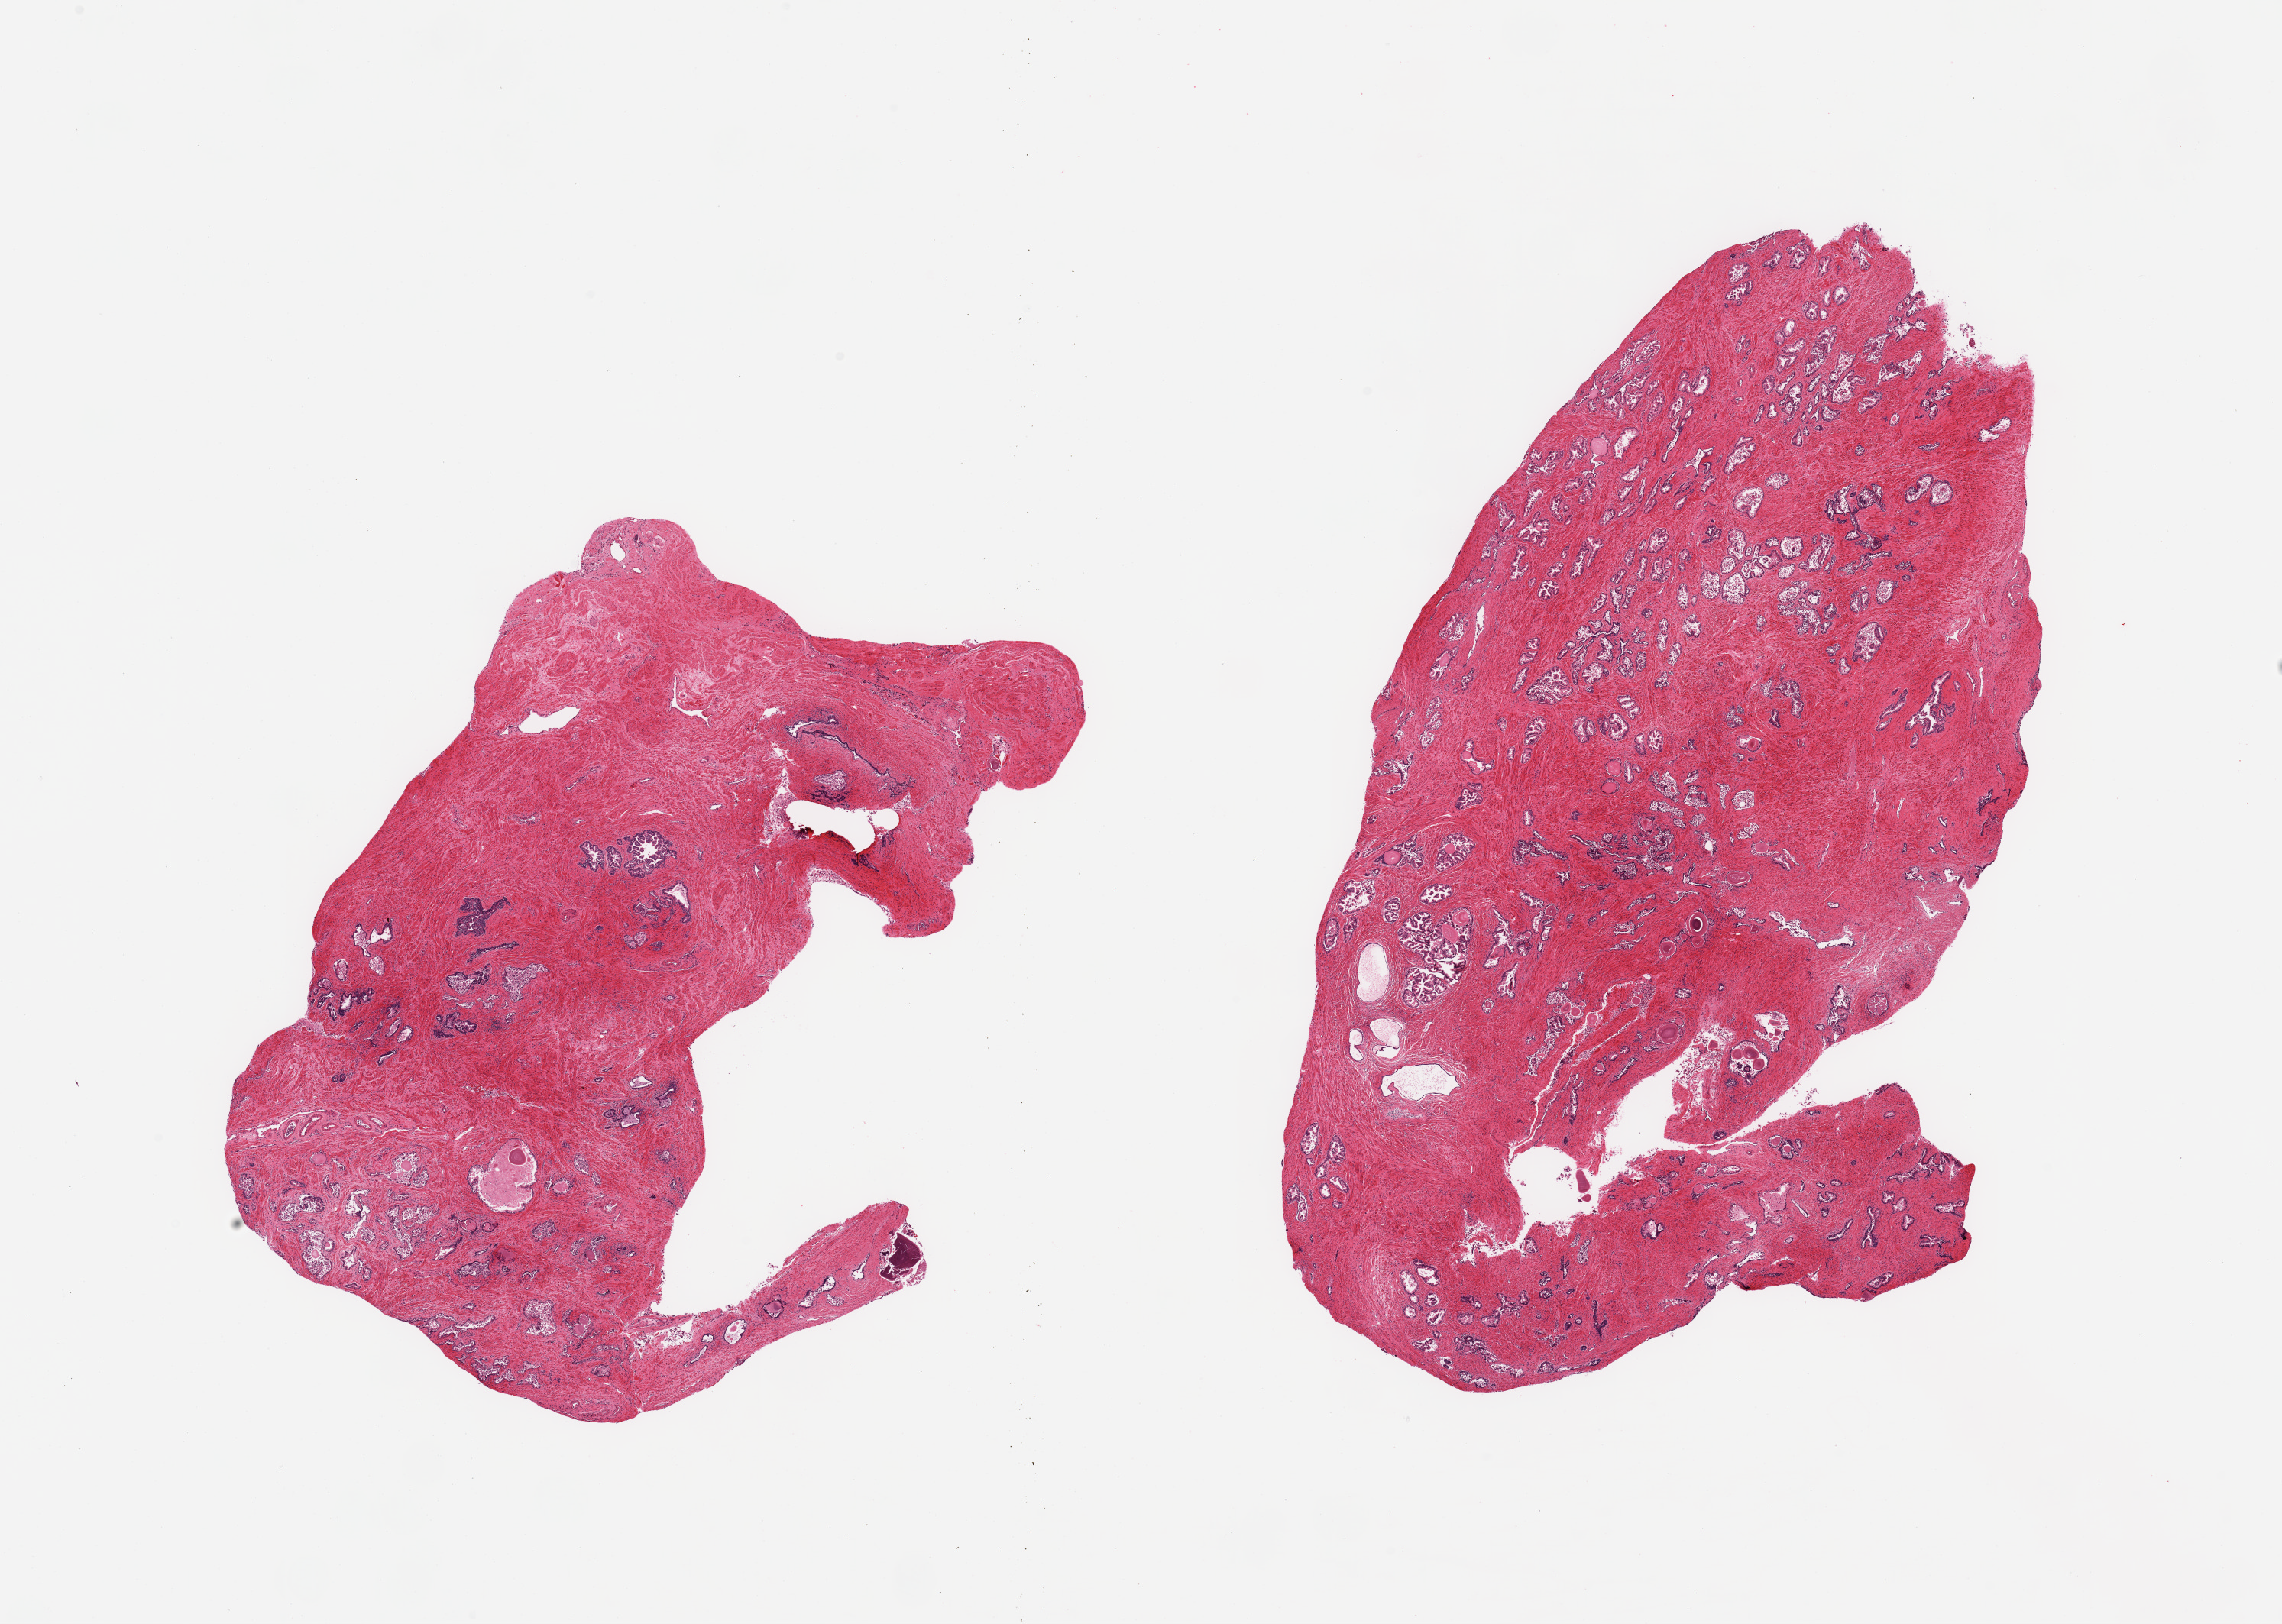
Digitized hematoxylin and eosin (H&E)-stained section, a low-resolution overview of the entire scanned area, about 23.6 x 16.8 mm (acquisition: 20x scan). PAXgene-fixed, paraffin-embedded tissue. Sampled site (target tissue): prostate. Donor tissue sample. Donor sex: male.
Reviewer comment on this tissue sample: 2 pieces; admixed glands and fibromuscular stroma, some sloughing of epithelium.